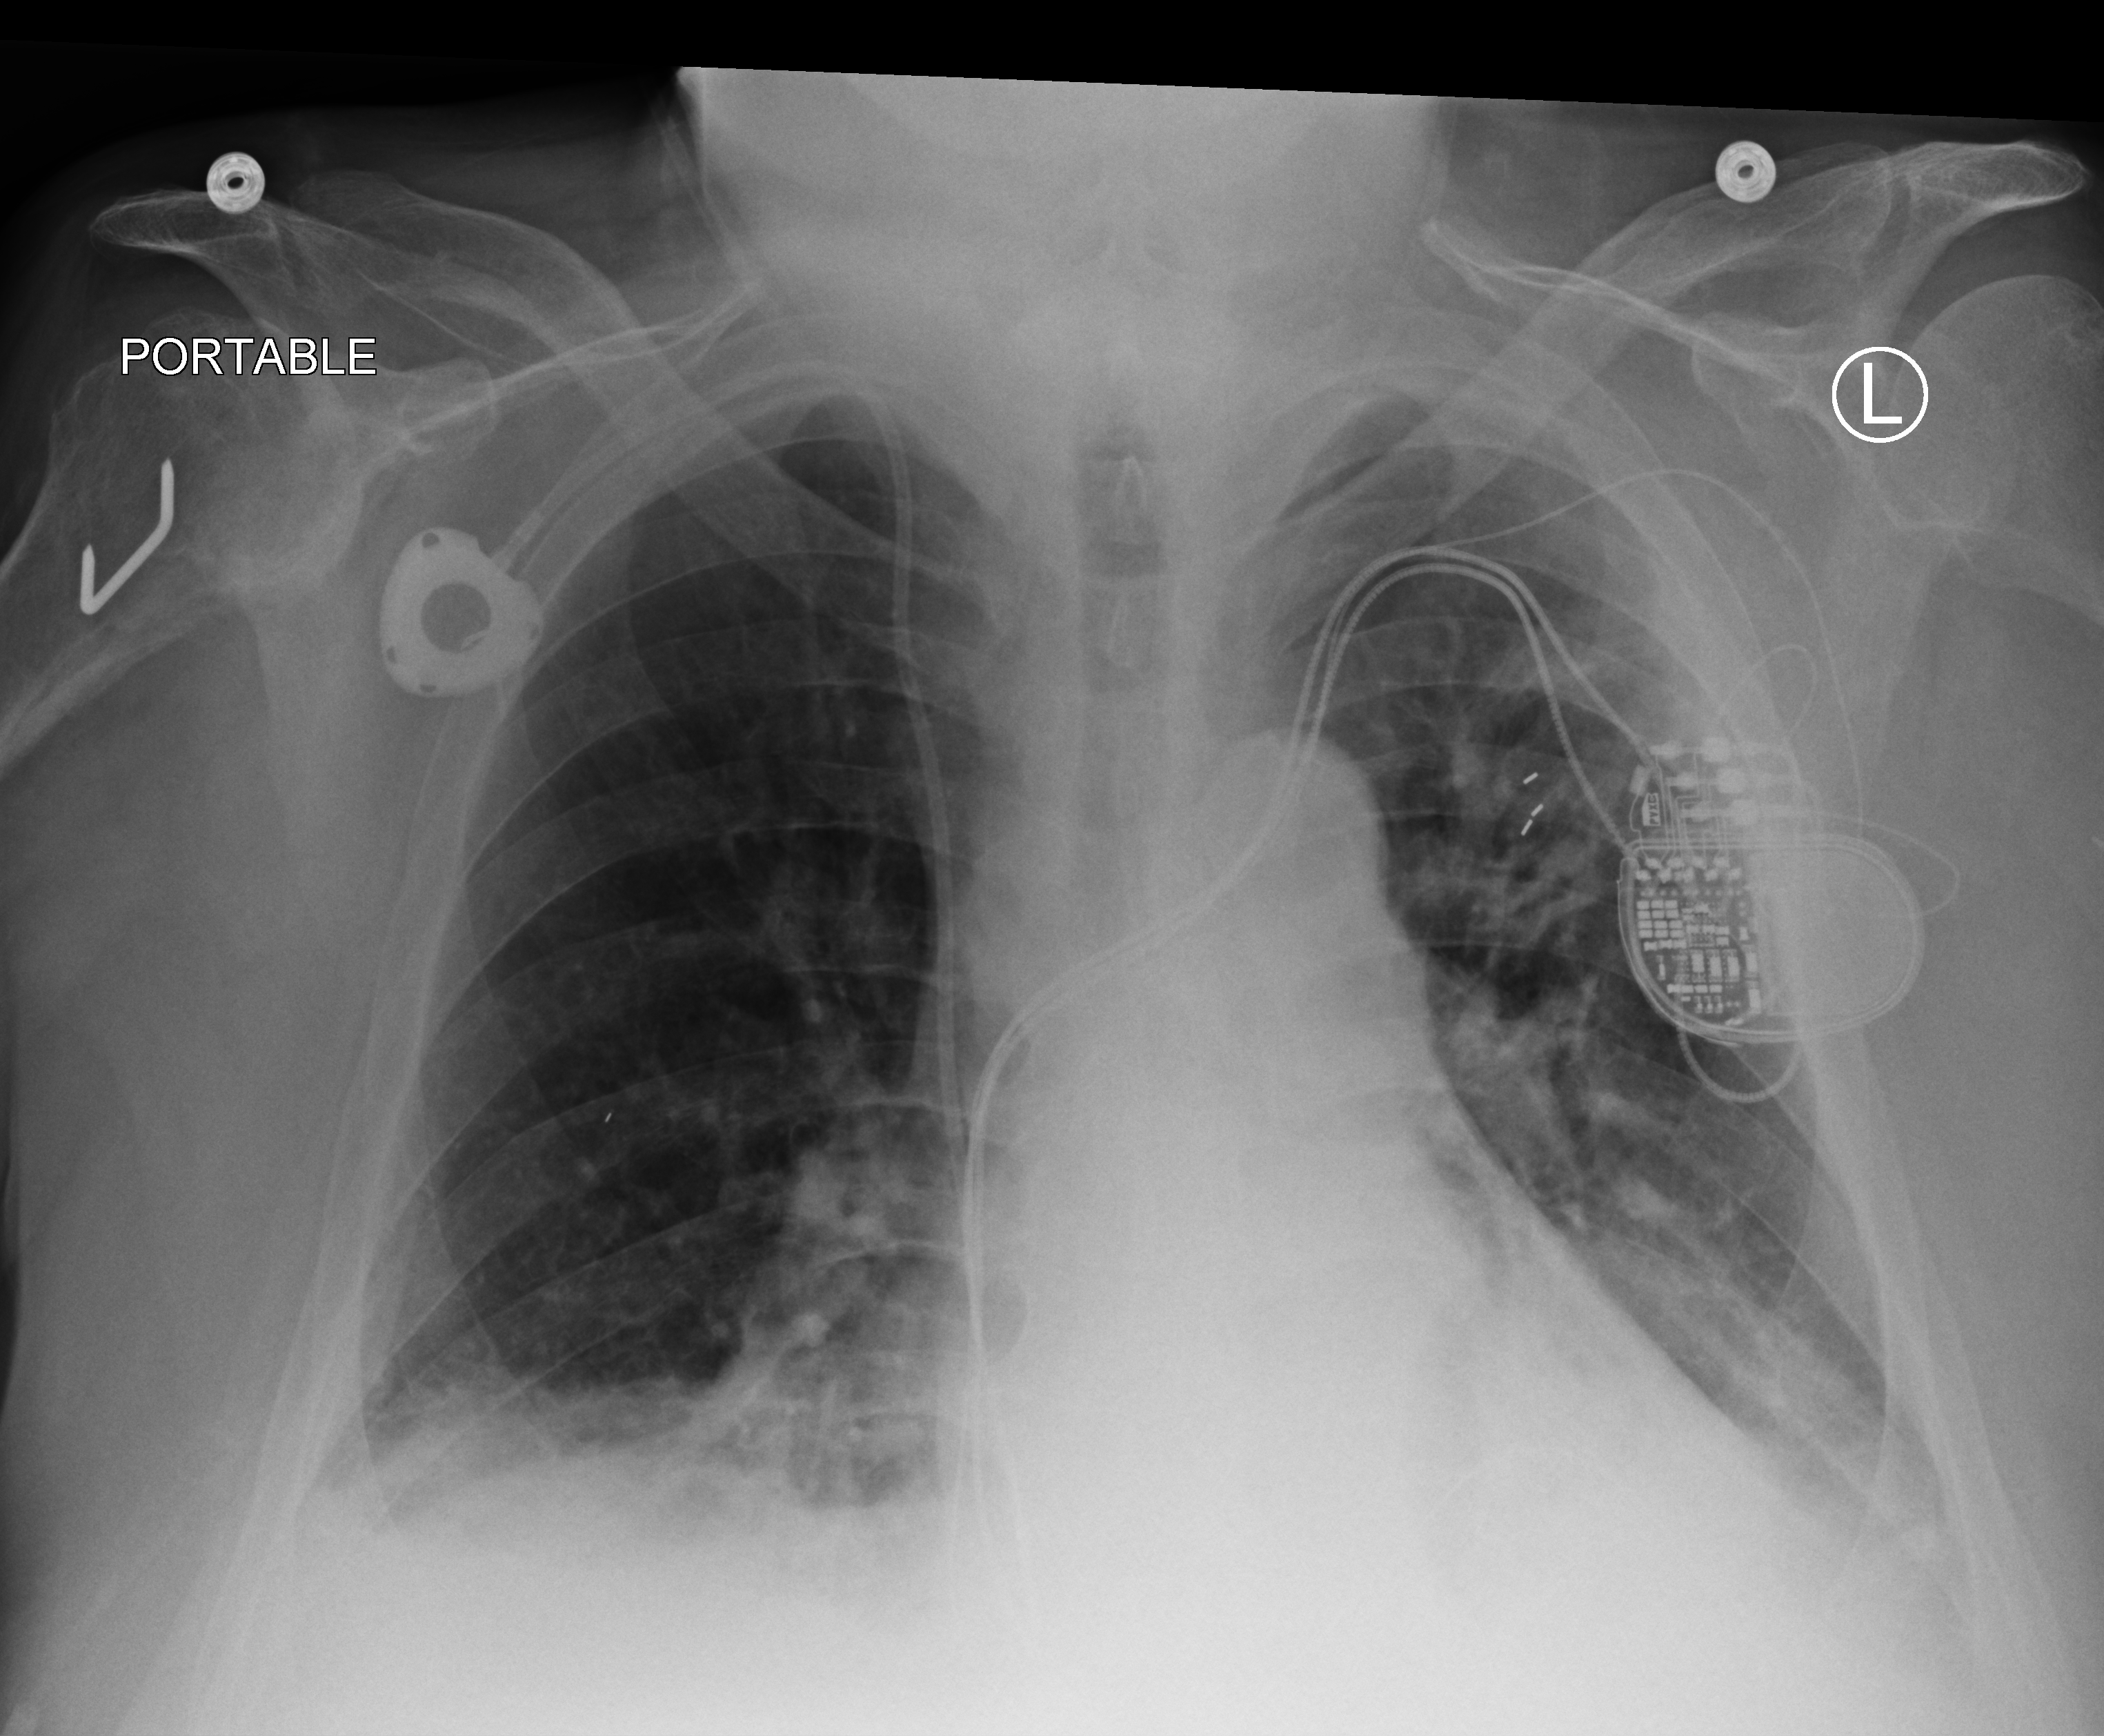
Portable chest radiograph, anteroposterior (AP) projection. Male patient hospitalised with COVID-19, age 60–74 years.
Admission-level facts for this patient (not findings on this image; timing relative to this image not recorded): mechanically ventilated during this hospital stay: no; admitted to intensive care during this hospital stay: yes.